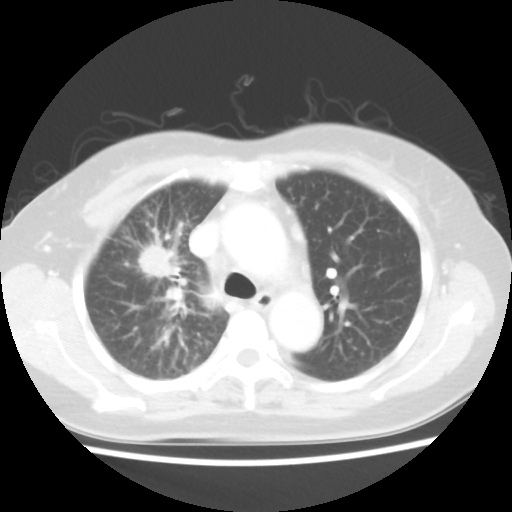
Chest CT, one axial slice; reconstruction kernel STANDARD; 100 kVp; lung window (W 1500 / L -600 HU); 5 mm slice thickness; 512 × 512 image matrix, field of view 312 × 312 mm. Female patient, age 55 years. Case-level facts recorded for this patient, not image findings: clinical TNM (as recorded): T1b N3 M1a.
Outlined on this slice (bounding box drawn by a radiologist):
- lung tumour (recorded histology: adenocarcinoma): bounding box <139,246,180,276> (left, top, right, bottom; pixels)